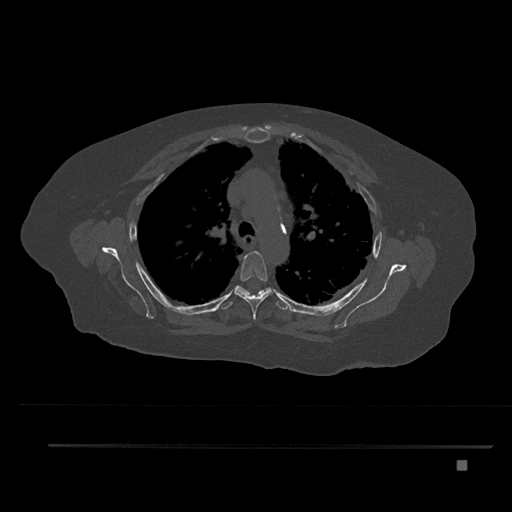
CT including the spine, one axial slice; position 594 of 797 along the scan axis; reconstruction kernel Br40s/3; 120 kVp; bone window (W 1800 / L 400 HU); 0.5 mm slice thickness; 512 × 512 image matrix, field of view 437 × 437 mm. Patient: female, 76 years. Case-level facts recorded for this patient, not image findings: primary cancer: lung; vertebrae with lytic lesions (as recorded): T11, L3.
Annotated regions visible in this slice (semi-automatically segmented with operator editing):
- T4 vertebra: box from (x=234, y=251) to (x=272, y=320) px
- T5 vertebra: (x=222, y=286)–(x=289, y=310)